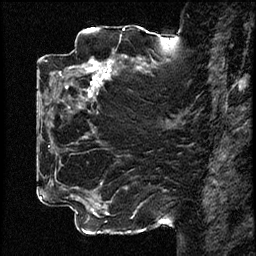
Breast MRI (dynamic contrast-enhanced), one sagittal slice; slice 38 of 78 in the series (ordered by position); dynamic contrast-enhanced study with each time point stored as its own series, time point 2 of 3 at this slice position (early post-contrast, ordered by acquisition time); 1.5 T; TE 4.2 ms, TR 17.6 ms; 2 mm slice thickness; 256 × 256 image matrix, field of view 200 × 200 mm. Patient: female, 42 years. From the clinical record (not read from this slice): setting: breast cancer imaged before/during neoadjuvant chemotherapy; receptor status: HER2-positive.
Annotated regions visible in this slice (semi-automatic segmentation, software-assisted and operator-edited):
- analysis volume of interest (the breast-tissue region the enhancement analysis was run in; not a lesion): bounding box <50,48,131,129> (left, top, right, bottom; pixels)
- tumour enhancement mask (voxels above the 100 % enhancement threshold inside the analysis volume of interest): <66,59,113,98>